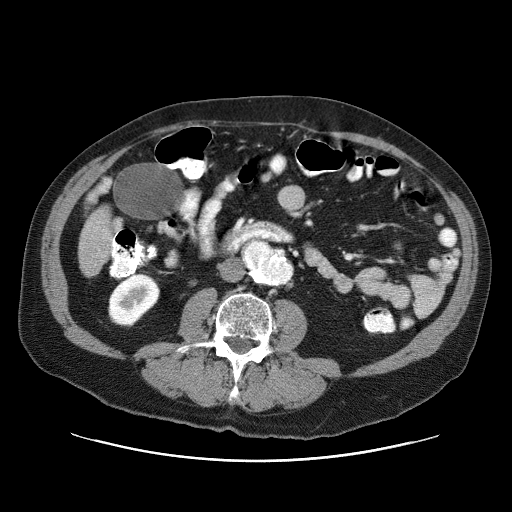
Contrast-enhanced abdominal CT (liver protocol), one axial slice. Slice 4 of 87 in the series (ordered by position). Reconstruction kernel STANDARD. 120 kVp. One of 3 acquisitions stored at this slice position. Soft-tissue window (W 400 / L 40 HU). 2.5 mm slice thickness. 512 × 512 image matrix, field of view 400 × 400 mm. Case-level facts recorded for this patient, not image findings: diagnosis: hepatocellular carcinoma (patient treated with transarterial chemoembolisation; whether this scan precedes or follows treatment is not stated here); TNM stage (as recorded): Stage-IIIA; Child-Pugh class: A; tumour differentiation: well differentiated; tumour nodularity: multinodular.
Structures marked on this image (semi-automatically segmented with operator editing):
- liver parenchyma outside the tumour (the mass and vessels are separate outlines, so this box may not span the whole liver): box from (x=78, y=178) to (x=112, y=276) px
- liver vessels: (x=102, y=182)–(x=108, y=190)